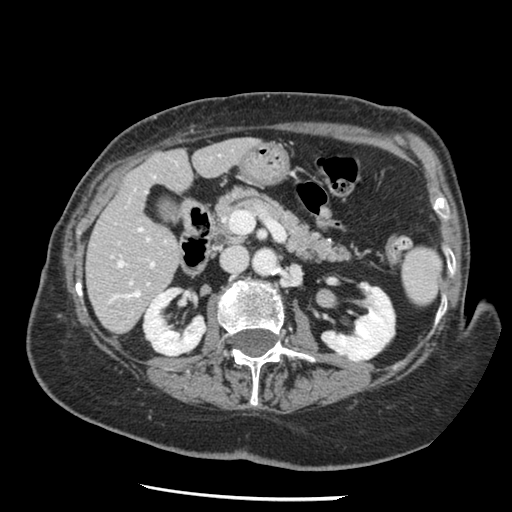
Contrast-enhanced abdominal CT, one axial slice; position 60 of 148 along the scan axis; 120 kVp; intravenous contrast given; soft-tissue window (W 400 / L 40 HU); 512 × 512 image matrix, field of view 330 × 330 mm. Female patient, age 85 years. From the clinical record (not read from this slice): diagnosis: colorectal cancer liver metastases, imaged before liver resection; multiple liver metastases: no; largest metastasis: 0.9 cm; disease in both lobes: no.
Annotated regions visible in this slice (expert manual segmentation):
- hepatic veins: bounding box <113,228,148,299> (left, top, right, bottom; pixels)
- liver: <87,139,254,333>
- planned liver remnant (the part of the liver to remain after resection): <87,139,254,322>
- portal vein (with intrahepatic branches): <151,263,154,266>